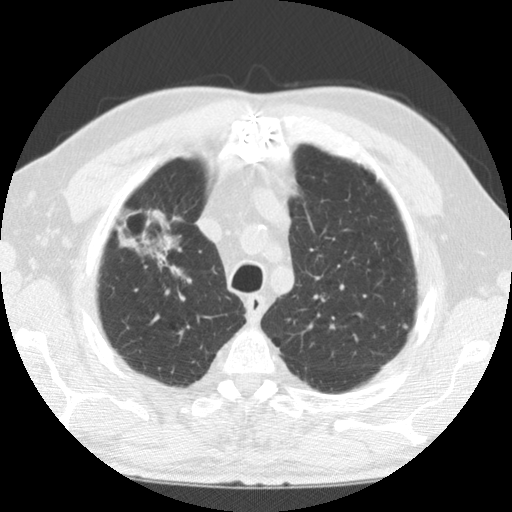
Low-dose screening chest CT, axial slice, baseline screening round, lung window (W 1500 / L -600 HU), 2.5 mm slice thickness, standard (soft-tissue) reconstruction kernel (STANDARD), 120 kVp, 512 × 512 image matrix. Male participant, aged 69 years at enrolment. Former smoker at enrolment.
• Expert reader's lesion annotation, box from (x=103, y=208) to (x=196, y=292) px.
• No non-calcified nodule or mass ≥4 mm was recorded by the screening reader at this exam.
• Official screen result: negative screen, minor abnormalities not suspicious for lung cancer.
• Participant outcome: lung cancer diagnosed 171 days after this screen — adenocarcinoma, NOS, right upper lobe, poorly differentiated (G3), stage IIIB (AJCC 6th edition), 40 mm at pathology.